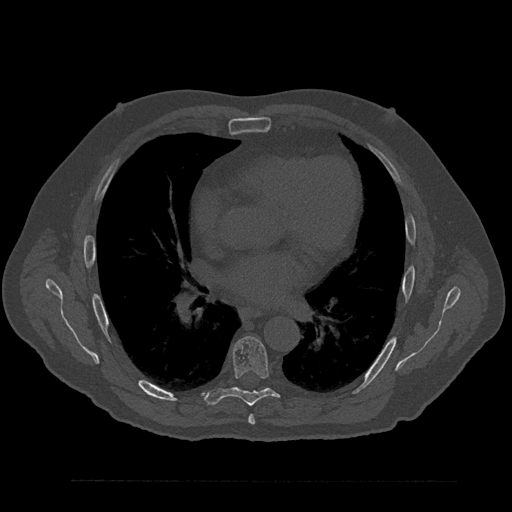
CT including the spine, one axial slice. Position 506 of 797 along the scan axis. Reconstruction kernel Br40s/3. 120 kVp. Bone window (W 1800 / L 400 HU). 0.5 mm slice thickness. 512 × 512 image matrix, field of view 430 × 430 mm. Patient: male, 61 years. From the clinical record (not read from this slice): primary cancer: prostate.
Outlined on this slice (semi-automatically segmented with operator editing):
- T6 vertebra: bounding box <248,415,255,425> (left, top, right, bottom; pixels)
- T7 vertebra: <204,336,279,406>